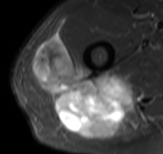
MRI of an extremity soft-tissue mass, one axial slice; position 61 of 61 along the scan axis; STIR; MR volume resampled by the dataset authors to the PET/CT grid (not the native acquisition matrix); 3.27 mm slice thickness; 163 × 154 image matrix, field of view 159 × 150 mm. Male patient. Case-level facts recorded for this patient, not image findings: histological type: poorly differentiated synovial sarcoma; grade: high; site of the primary tumour: right buttock.
Structures marked on this image (expert contour drawn on MRI and transferred to this co-registered scan by the dataset authors):
- gross tumour volume including surrounding oedema: box from (x=32, y=37) to (x=147, y=140) px
- gross tumour volume (mass): (x=32, y=37)–(x=133, y=138)